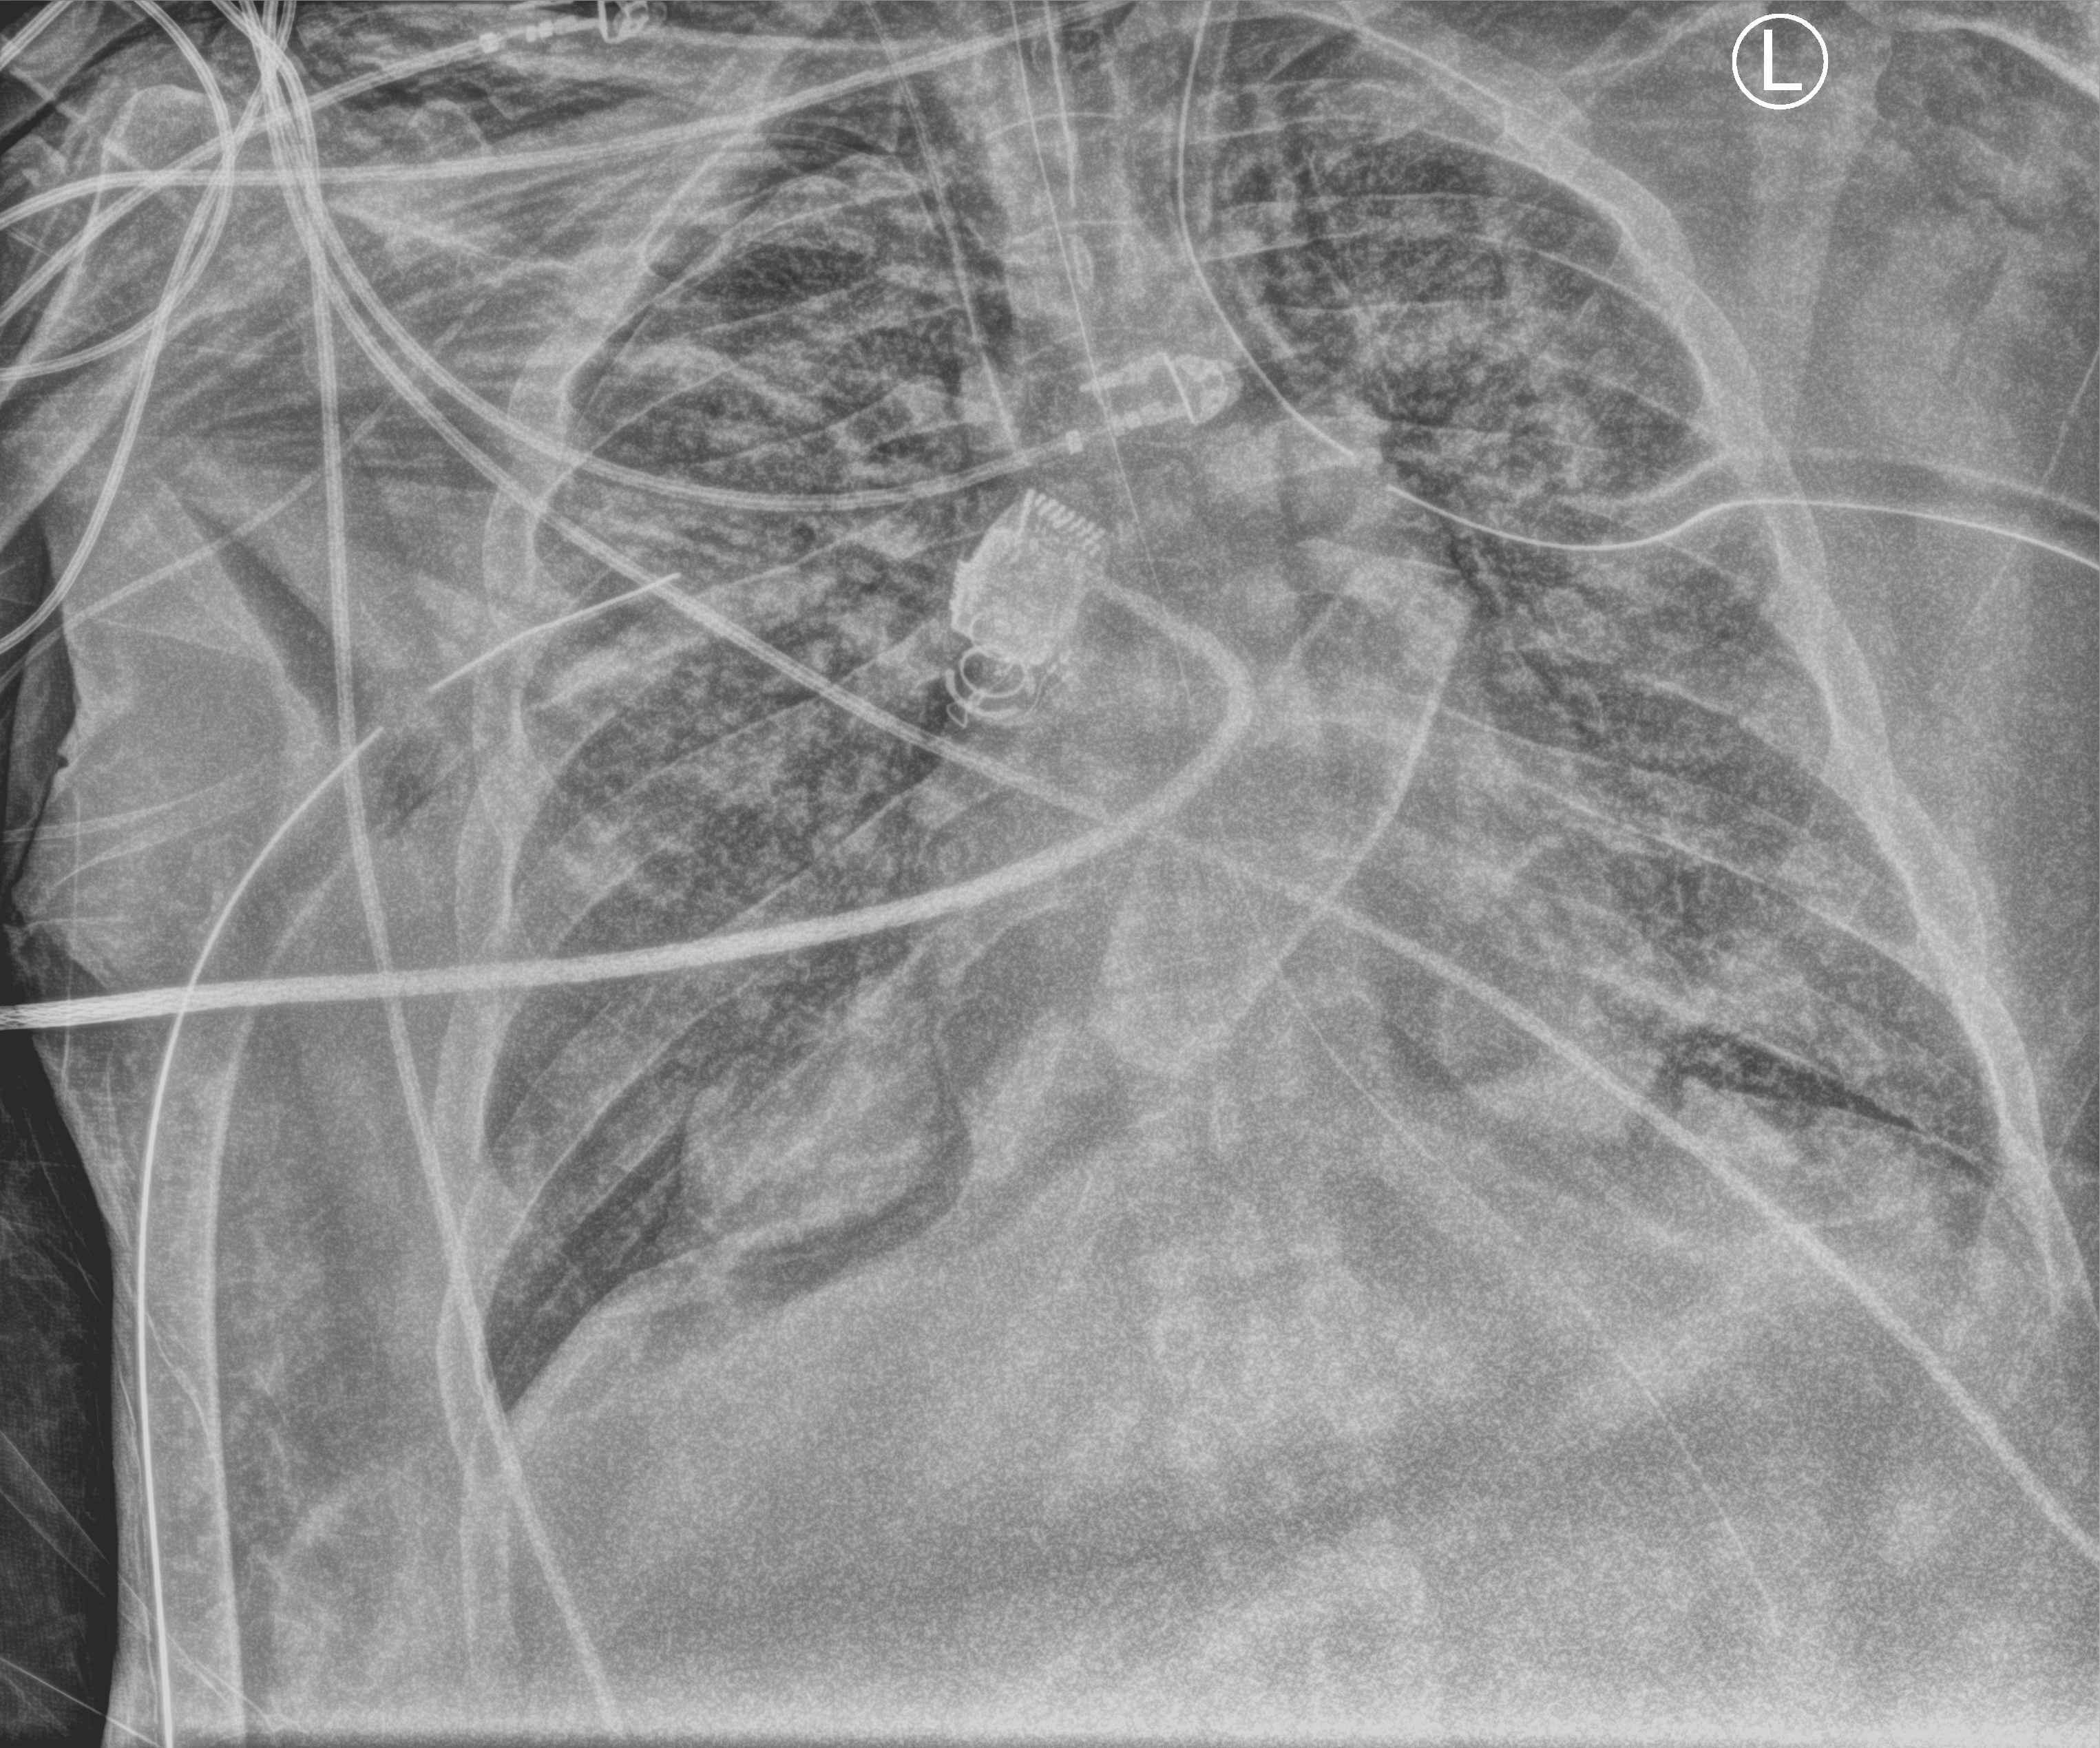
Portable chest radiograph; anteroposterior (AP) projection. Patient hospitalised with COVID-19, aged 18–59 years.
Hospital-stay facts (about this admission, not read from this image; timing relative to this image not recorded): admitted to intensive care during this hospital stay: yes.